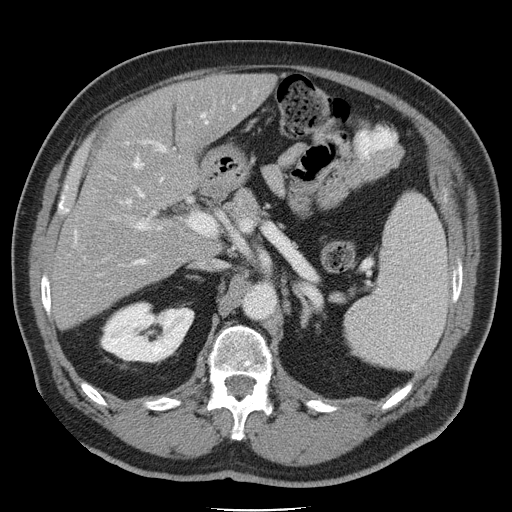
Contrast-enhanced abdominal CT, one axial slice. Slice 25 of 45 in the series (ordered by position). Intravenous contrast given. Soft-tissue window (W 400 / L 40 HU). 5 mm slice thickness. 512 × 512 image matrix, field of view 386 × 386 mm. Male patient, age 65 years. Case-level facts recorded for this patient, not image findings: diagnosis: colorectal cancer liver metastases, imaged before liver resection; multiple liver metastases: yes; largest metastasis: 4.9 cm; chemotherapy before resection: yes.
Structures marked on this image (outlined manually by an expert reader):
- hepatic veins: bounding box (x1, y1, x2, y2) in pixels: (132, 105, 236, 264)
- liver: (53, 75, 272, 326)
- planned liver remnant (the part of the liver to remain after resection): (103, 75, 271, 203)
- portal vein (with intrahepatic branches): (110, 113, 228, 241)